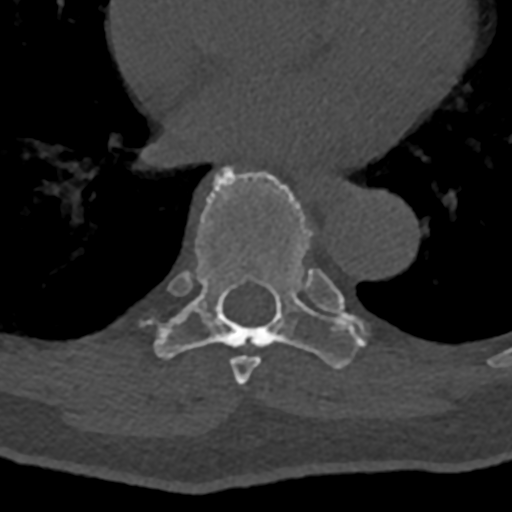
CT including the spine, one axial slice; position 721 of 797 along the scan axis; 120 kVp; bone window (W 1800 / L 400 HU); 0.5 mm slice thickness; 512 × 512 image matrix. Patient: male, 74 years. From the clinical record (not read from this slice): primary cancer: renal.
Annotated regions visible in this slice (semi-automatically segmented with operator editing):
- T7 vertebra: bounding box [x1, y1, x2, y2] px = [230, 269, 341, 385]
- T8 vertebra: [155, 164, 366, 369]